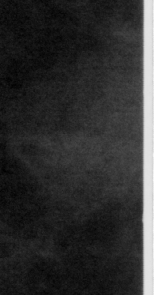
Crop from a digitized film mammogram around one marked abnormality, right breast, CC view, BI-RADS breast density category 2 (scale 1–4).
Marked abnormality: mass, shape round, margins circumscribed; BI-RADS assessment category 3; benign; no additional work-up was recommended (benign without callback).